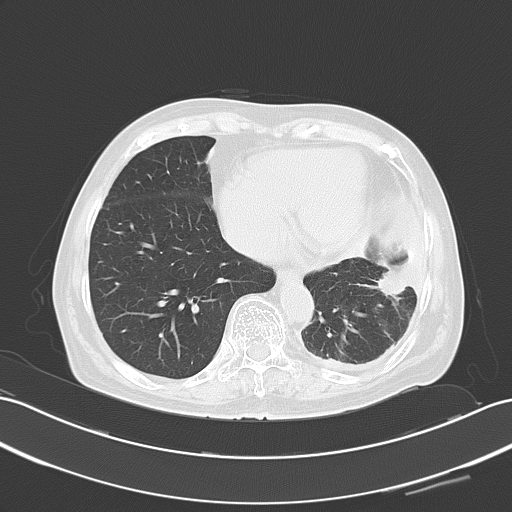
Chest CT, one axial slice; position 20 of 60 along the scan axis; reconstruction kernel B70f; lung window (W 1500 / L -600 HU); 5 mm slice thickness; 512 × 512 image matrix, field of view 353 × 353 mm. Patient: female, 82 years. Case-level facts recorded for this patient, not image findings: clinical TNM (as recorded): T1c N0 M1.
Outlined on this slice (bounding box drawn by a radiologist):
- lung tumour (recorded histology: adenocarcinoma): bounding box [x1, y1, x2, y2] px = [371, 266, 411, 300]